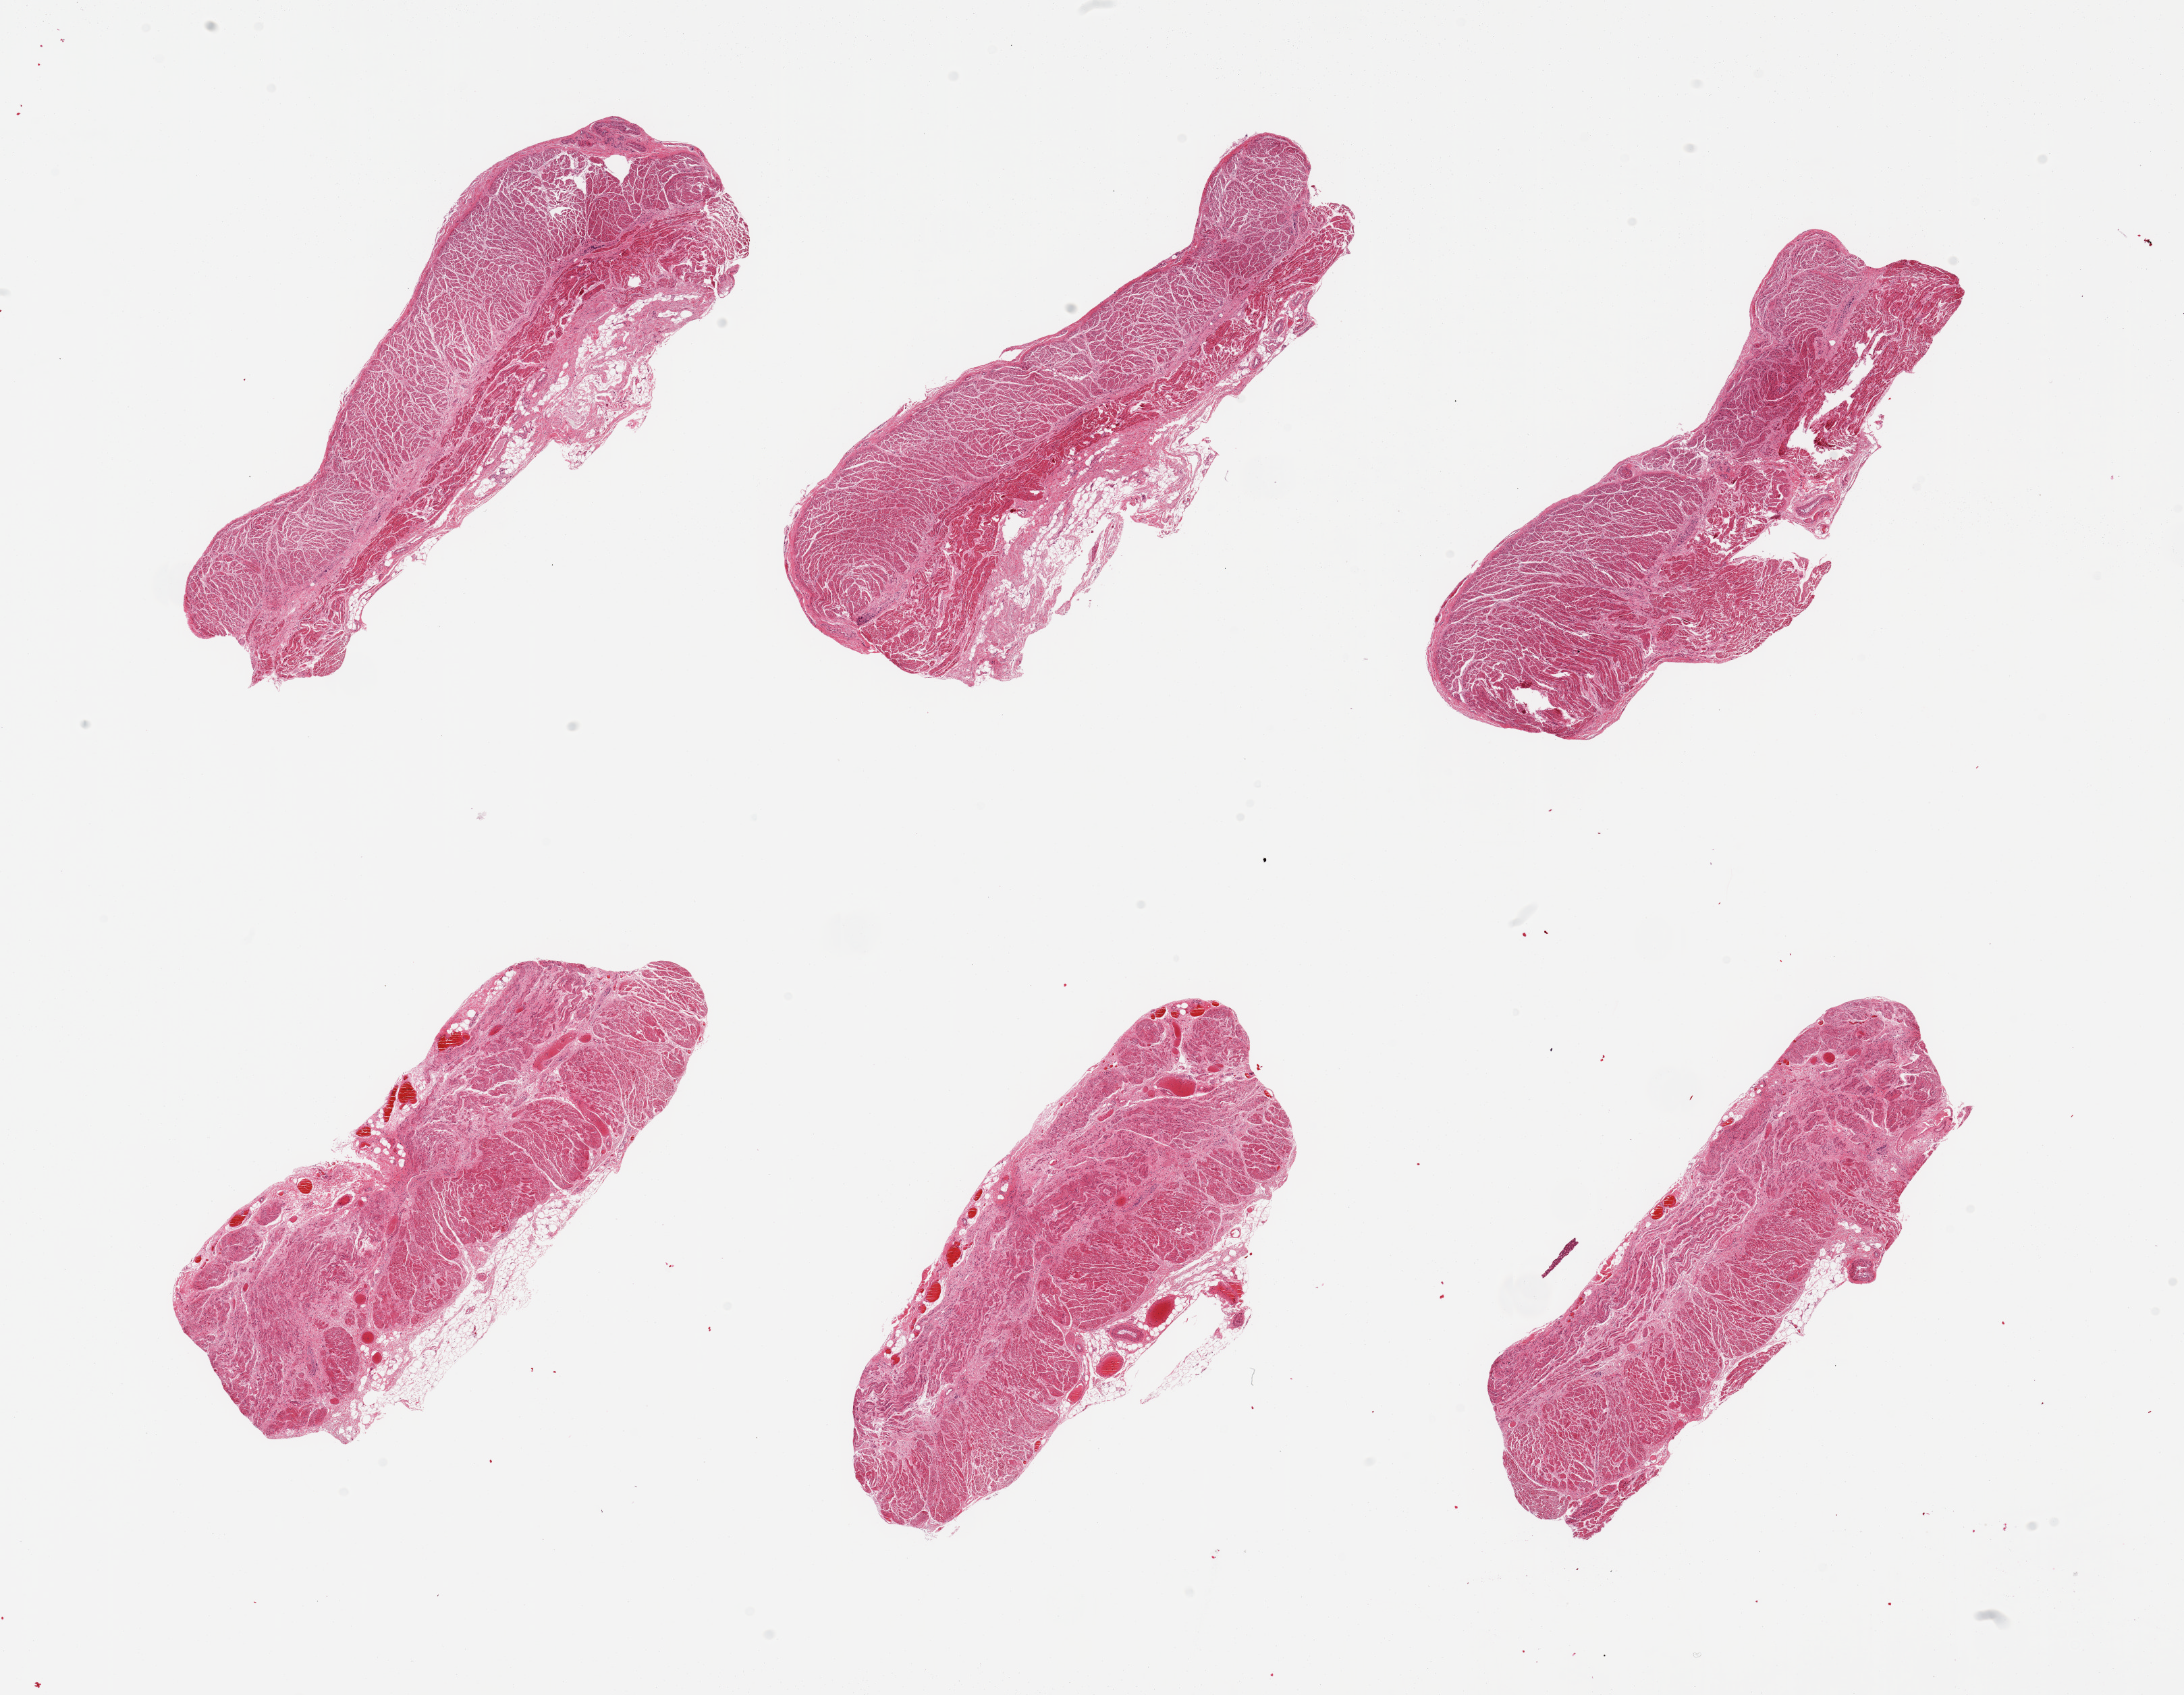
Hematoxylin and eosin (H&E) whole-slide image, brightfield, a low-resolution overview of the entire scanned area, about 25.6 x 19.9 mm. PAXgene-fixed paraffin-embedded (PFPE) section. Sampled site (target tissue): gastroesophageal junction. Donor tissue sample. Male donor.
Review note (as recorded): 6 pieces, all muscularis, good specimens.